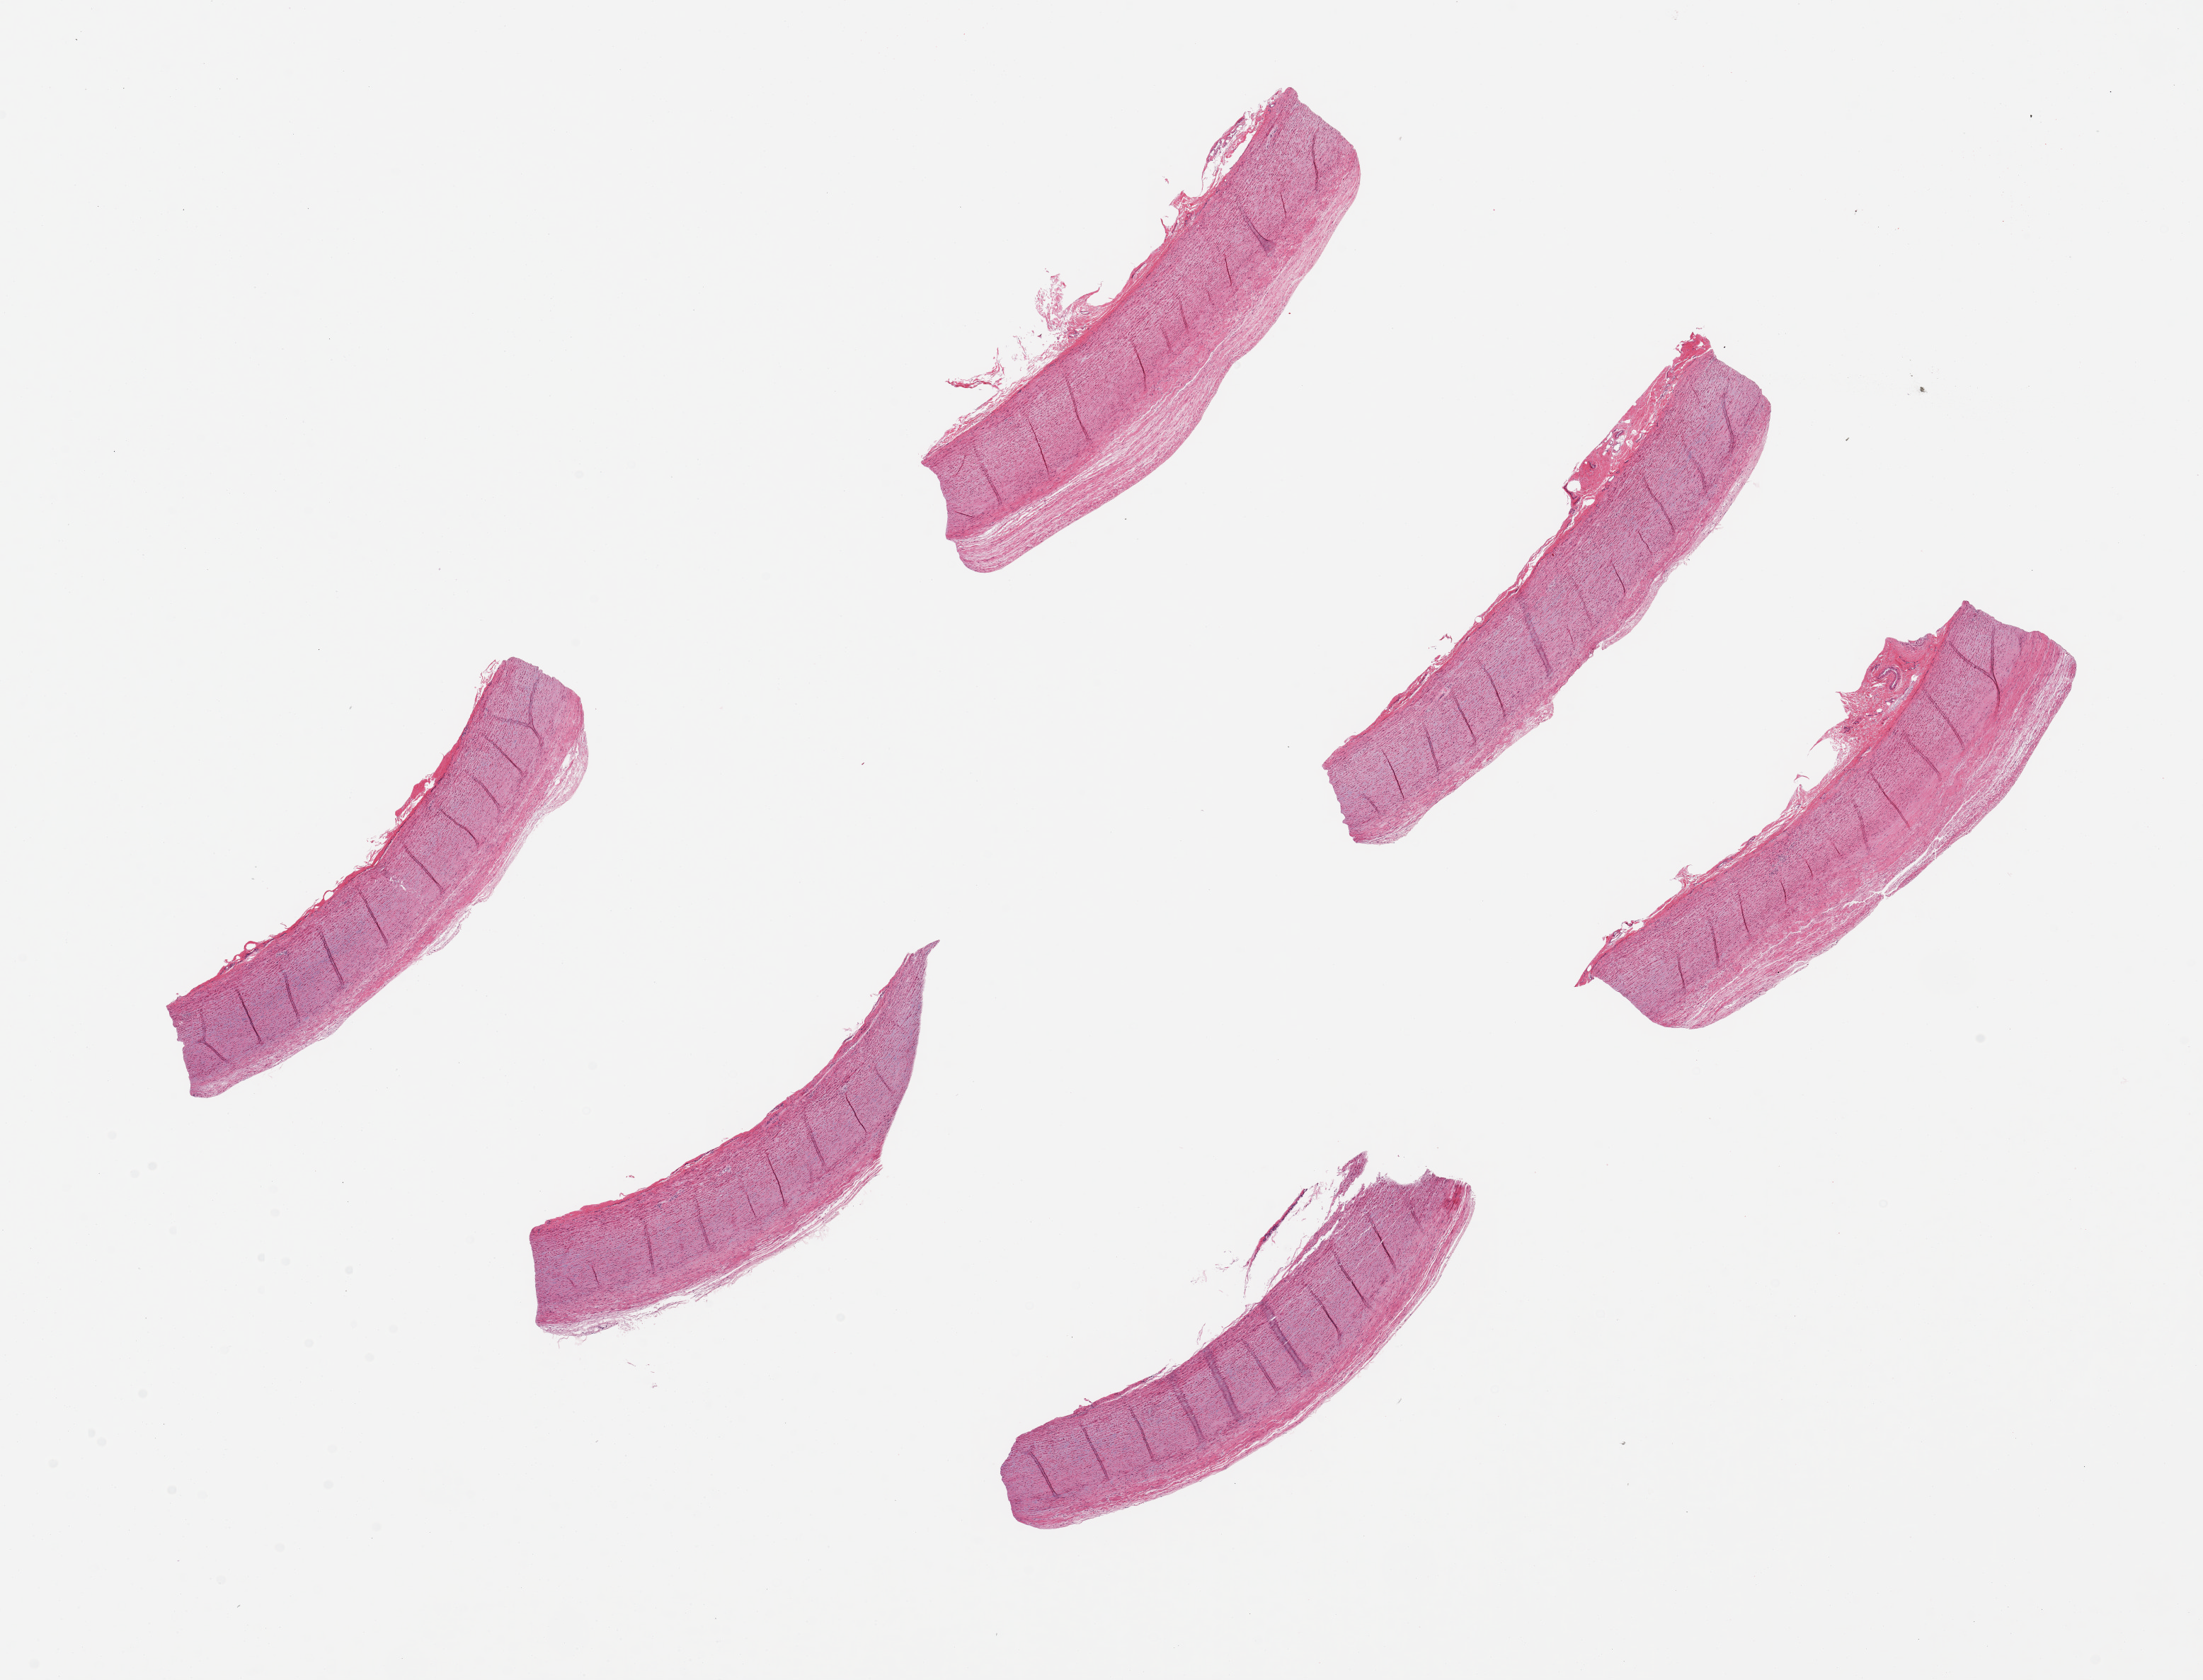
Digitized H&E-stained section, whole scanned area (about 24.6 x 18.8 mm, from a 20x scan) shown as a low-resolution overview; PAXgene-fixed, paraffin-embedded tissue; section of aorta (target tissue); tissue donor sample. Donor: male.
Reviewer comment on this tissue sample: 6 pieces, up to 7x1mm; no lesions.